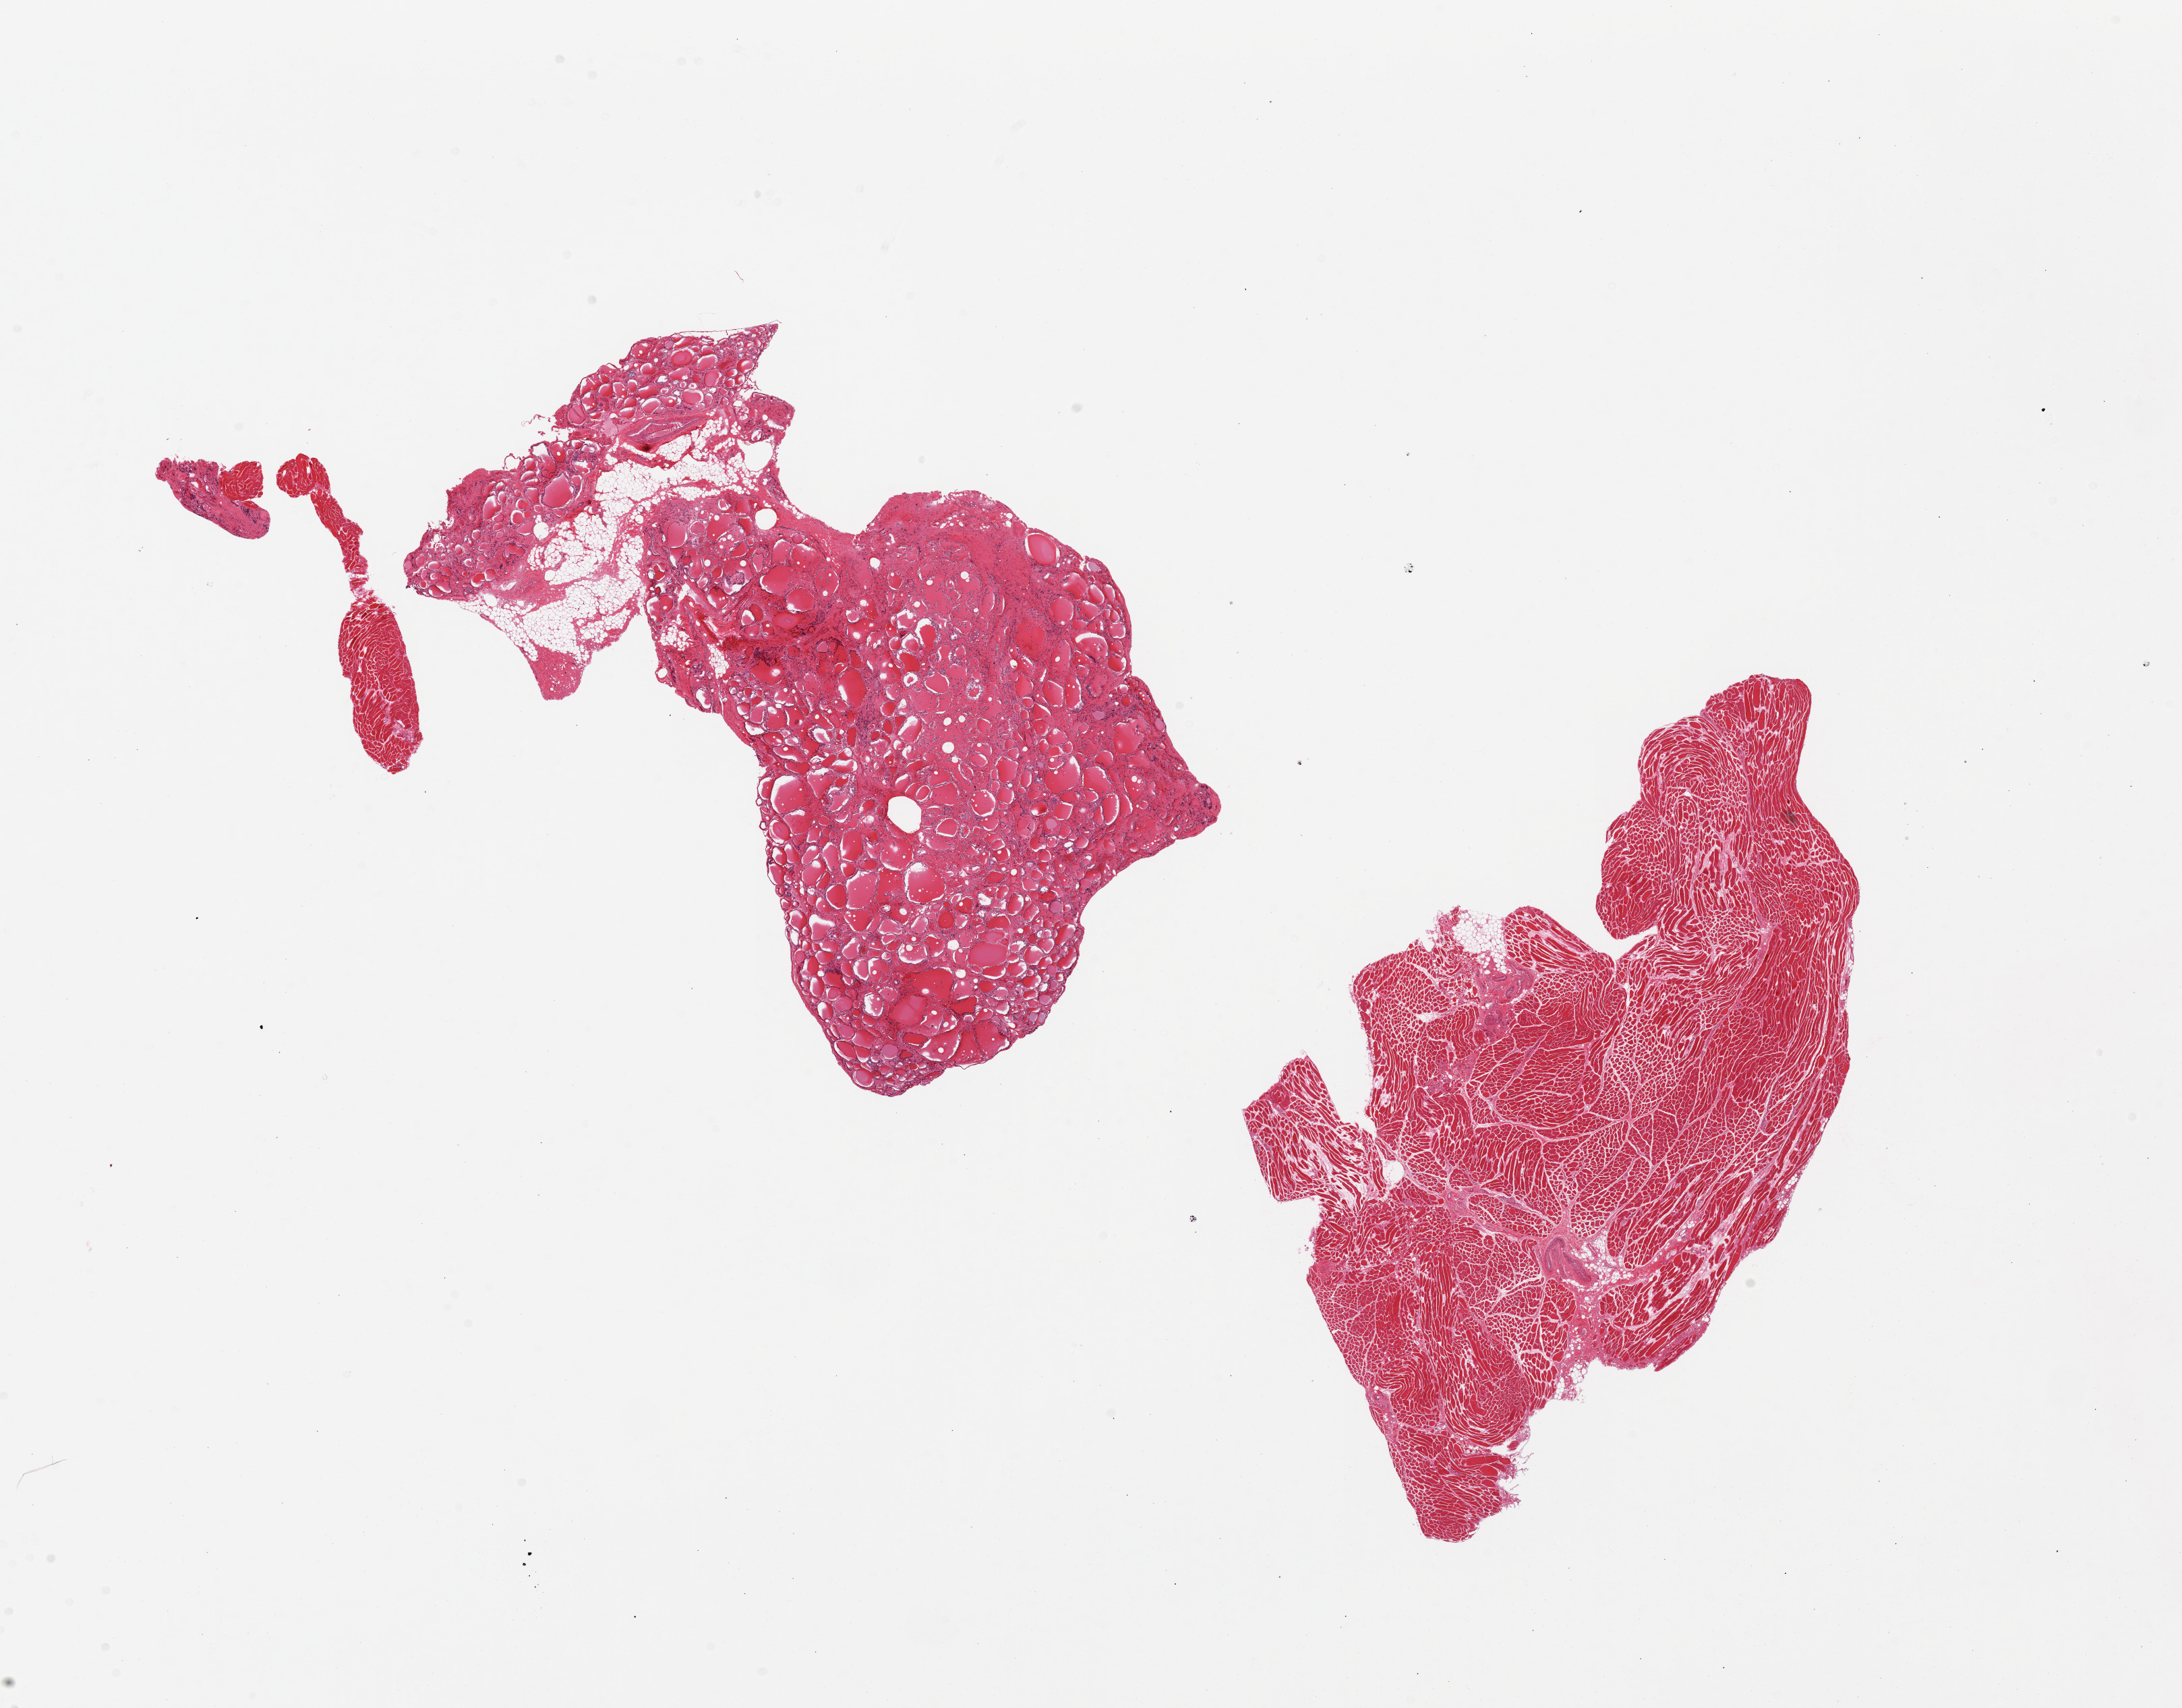
Whole-slide image, haematoxylin and eosin stain, brightfield, shown as a low-resolution overview of the whole scanned area (about 25.6 x 20.0 mm, acquisition: 20x scan), PAXgene-fixed paraffin-embedded (PFPE) section, target tissue: thyroid, tissue donor sample. Male donor.
Review note (as recorded): 3 pieces: largest and smallest pieces are skeletal muscle. Thyroid poorly preserved.